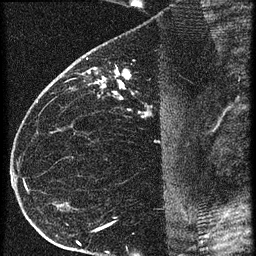
Breast MRI (dynamic contrast-enhanced), one sagittal slice; position 36 of 60 along the scan axis; 3 images stored at this slice position (order not interpretable as contrast timing); 1.5 T; TE 4.2 ms, TR 20.4 ms; 1.5 mm slice thickness; 256 × 256 image matrix, field of view 180 × 180 mm. Female patient, age 35 years. Case-level facts recorded for this patient, not image findings: setting: breast cancer imaged before/during neoadjuvant chemotherapy; receptor status: HR-positive, HER2-negative.
Structures marked on this image (semi-automatic segmentation, software-assisted and operator-edited):
- analysis volume of interest (the breast-tissue region the enhancement analysis was run in; not a lesion): bounding box [x1, y1, x2, y2] px = [65, 60, 169, 119]
- tumour enhancement mask (voxels above the 90 % enhancement threshold inside the analysis volume of interest): [89, 68, 149, 117]